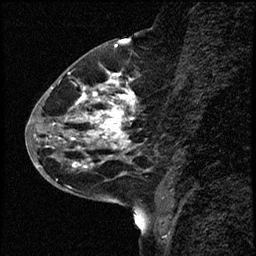
Breast MRI (dynamic contrast-enhanced), one sagittal slice; slice 25 of 68 in the series (ordered by position); dynamic contrast-enhanced study with each time point stored as its own series, time point 2 of 3 at this slice position (early post-contrast, ordered by acquisition time); 1.5 T; TE 4.2 ms, TR 17.6 ms; 2 mm slice thickness; 256 × 256 image matrix, field of view 200 × 200 mm. Patient: female, 52 years. From the clinical record (not read from this slice): setting: breast cancer imaged before/during neoadjuvant chemotherapy; receptor status: HER2-positive.
Outlined on this slice (semi-automatic segmentation, software-assisted and operator-edited):
- analysis volume of interest (the breast-tissue region the enhancement analysis was run in; not a lesion): bounding box [x1, y1, x2, y2] px = [50, 61, 156, 184]
- tumour enhancement mask (voxels above the 100 % enhancement threshold inside the analysis volume of interest): [53, 73, 135, 168]